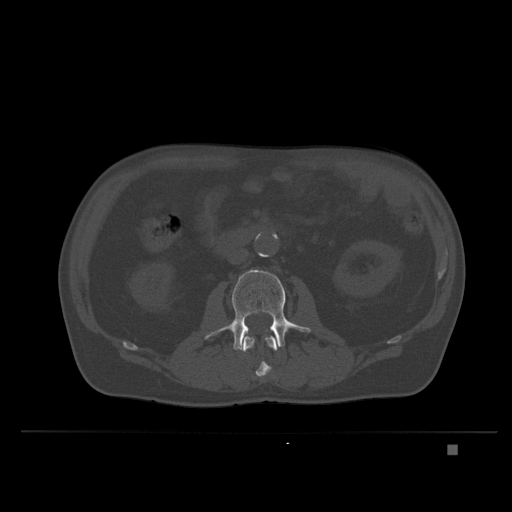
CT including the spine, one axial slice; slice 103 of 435 in the series (ordered by position); bone window (W 1800 / L 400 HU); 1.5 mm slice thickness; 512 × 512 image matrix, field of view 434 × 434 mm. Male patient, age 73 years. Case-level facts recorded for this patient, not image findings: primary cancer: skin.
Annotated regions visible in this slice (semi-automatic segmentation, software-assisted and operator-edited):
- L2 vertebra: bounding box (x1, y1, x2, y2) in pixels: (243, 333, 278, 381)
- L3 vertebra: (205, 269, 311, 351)